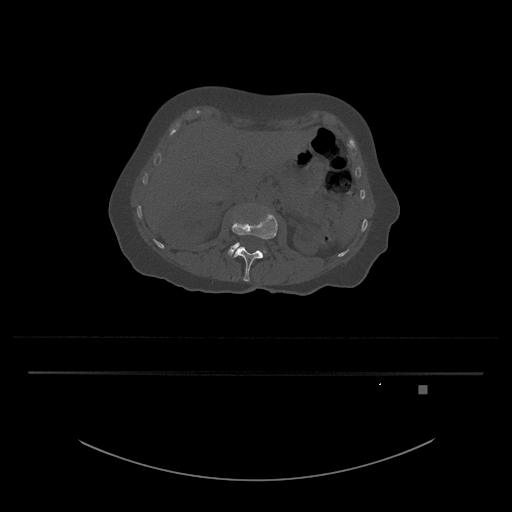
CT including the spine, one axial slice. Position 476 of 797 along the scan axis. Reconstruction kernel Br40s/3. 120 kVp. Bone window (W 1800 / L 400 HU). 0.5 mm slice thickness. 512 × 512 image matrix. Female patient, age 57 years. Case-level facts recorded for this patient, not image findings: primary cancer: cervical.
Annotated regions visible in this slice (semi-automatically segmented with operator editing):
- L3 vertebra: box from (x=228, y=242) to (x=266, y=256) px